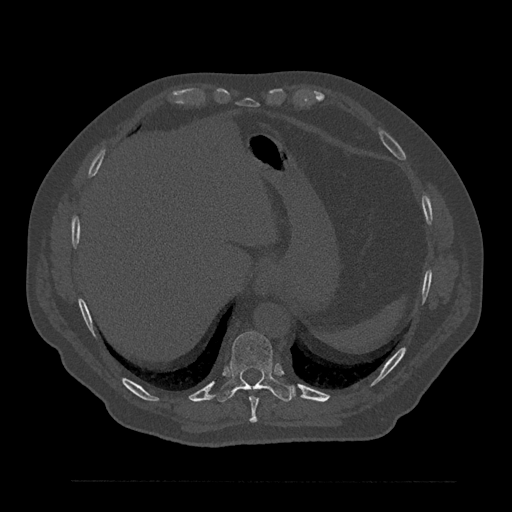
CT including the spine, one axial slice. Slice 366 of 797 in the series (ordered by position). Reconstruction kernel Br40s/3. 120 kVp. Bone window (W 1800 / L 400 HU). 512 × 512 image matrix. Male patient, age 61 years. From the clinical record (not read from this slice): primary cancer: prostate.
Outlined on this slice (semi-automatic segmentation, software-assisted and operator-edited):
- T10 vertebra: bounding box <216,331,294,402> (left, top, right, bottom; pixels)
- T9 vertebra: <249,396,259,423>